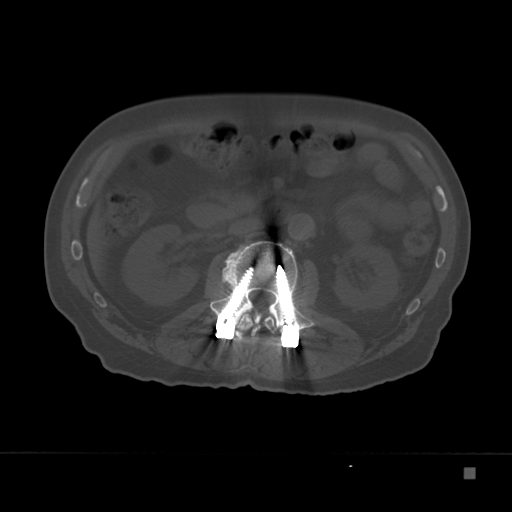
CT including the spine, one axial slice. Bone window (W 1800 / L 400 HU). 512 × 512 image matrix, field of view 389 × 389 mm. Patient: male, 72 years. Case-level facts recorded for this patient, not image findings: primary cancer: skeletal.
Annotated regions visible in this slice (semi-automatically segmented with operator editing):
- L1 vertebra: bounding box [x1, y1, x2, y2] px = [237, 308, 276, 334]
- L2 vertebra: [209, 241, 316, 331]